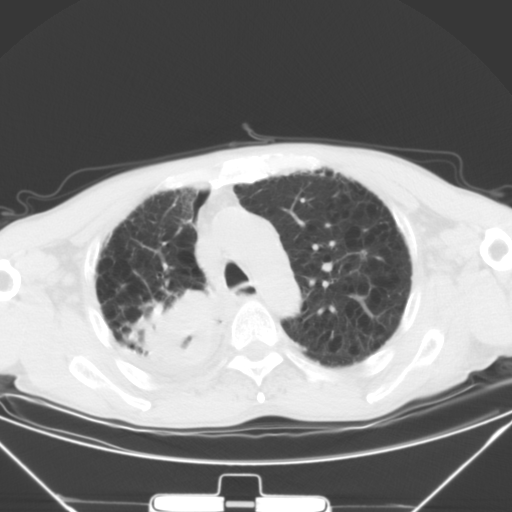
Chest CT, one axial slice; position 36 of 50 along the scan axis; 120 kVp; lung window (W 1500 / L -600 HU); 5 mm slice thickness; 512 × 512 image matrix, field of view 373 × 373 mm. Male patient, age 65 years. From the clinical record (not read from this slice): clinical TNM (as recorded): T3 N1 M1a.
Outlined on this slice (bounding box drawn by a radiologist):
- lung tumour (recorded histology: squamous cell carcinoma): bounding box [x1, y1, x2, y2] px = [142, 287, 221, 372]